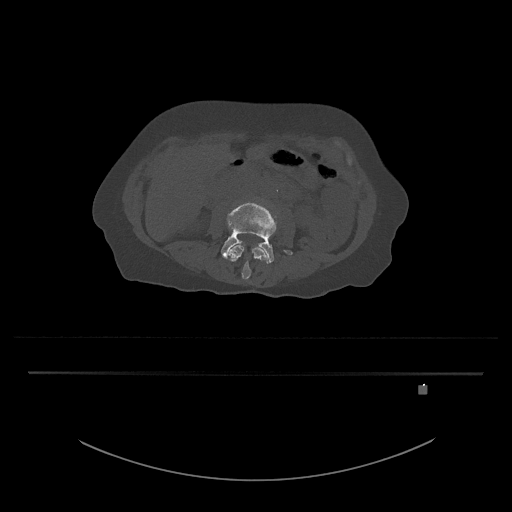
CT including the spine, one axial slice. Position 391 of 797 along the scan axis. 120 kVp. Bone window (W 1800 / L 400 HU). 0.5 mm slice thickness. 512 × 512 image matrix, field of view 500 × 500 mm. Patient: female, 57 years. Case-level facts recorded for this patient, not image findings: primary cancer: cervical.
Structures marked on this image (semi-automatic segmentation, software-assisted and operator-edited):
- L3 vertebra: bounding box <228,244,268,280> (left, top, right, bottom; pixels)
- L4 vertebra: <221,202,293,264>